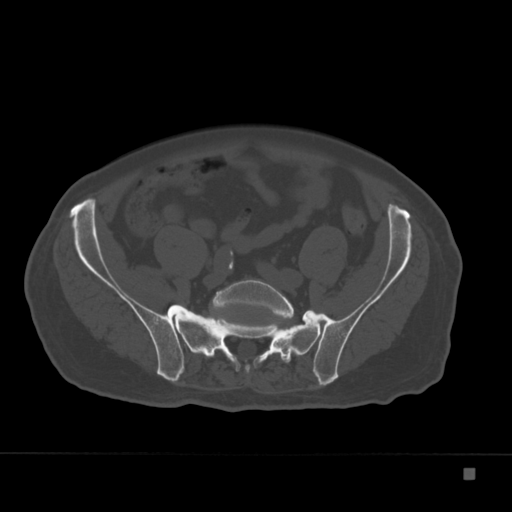
CT including the spine, one axial slice; slice 11 of 332 in the series (ordered by position); reconstruction kernel Br40s; bone window (W 1800 / L 400 HU); 1.5 mm slice thickness; 512 × 512 image matrix. Patient: male, 72 years. From the clinical record (not read from this slice): primary cancer: skeletal.
Structures marked on this image (semi-automatic segmentation, software-assisted and operator-edited):
- L5 vertebra: bounding box (x1, y1, x2, y2) in pixels: (212, 280, 294, 351)